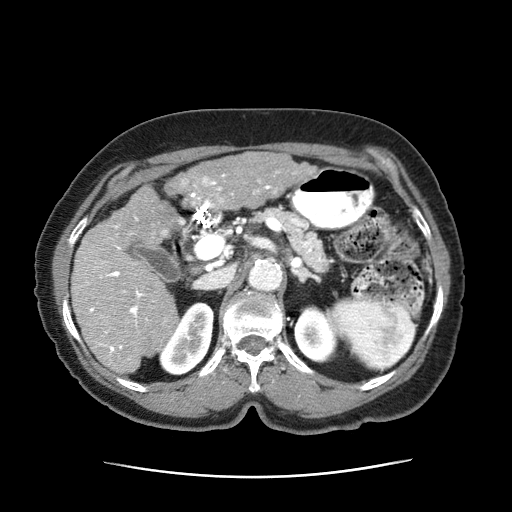
Contrast-enhanced abdominal CT (liver protocol), one axial slice. Slice 28 of 63 in the series (ordered by position). 120 kVp. Intravenous contrast given. Soft-tissue window (W 400 / L 40 HU). 2.5 mm slice thickness. 512 × 512 image matrix, field of view 360 × 360 mm. Patient: female, 79 years. From the clinical record (not read from this slice): diagnosis: hepatocellular carcinoma (patient treated with transarterial chemoembolisation; whether this scan precedes or follows treatment is not stated here); TNM stage (as recorded): Stage-II; Child-Pugh class: B; tumour differentiation: well differentiated; tumour size: 5 cm.
Structures marked on this image (semi-automatic segmentation, software-assisted and operator-edited):
- abdominal aorta: bounding box [x1, y1, x2, y2] px = [248, 255, 281, 292]
- liver parenchyma outside the tumour (the mass and vessels are separate outlines, so this box may not span the whole liver): [71, 185, 185, 377]
- mass: [162, 152, 317, 207]
- liver vessels: [82, 174, 270, 356]